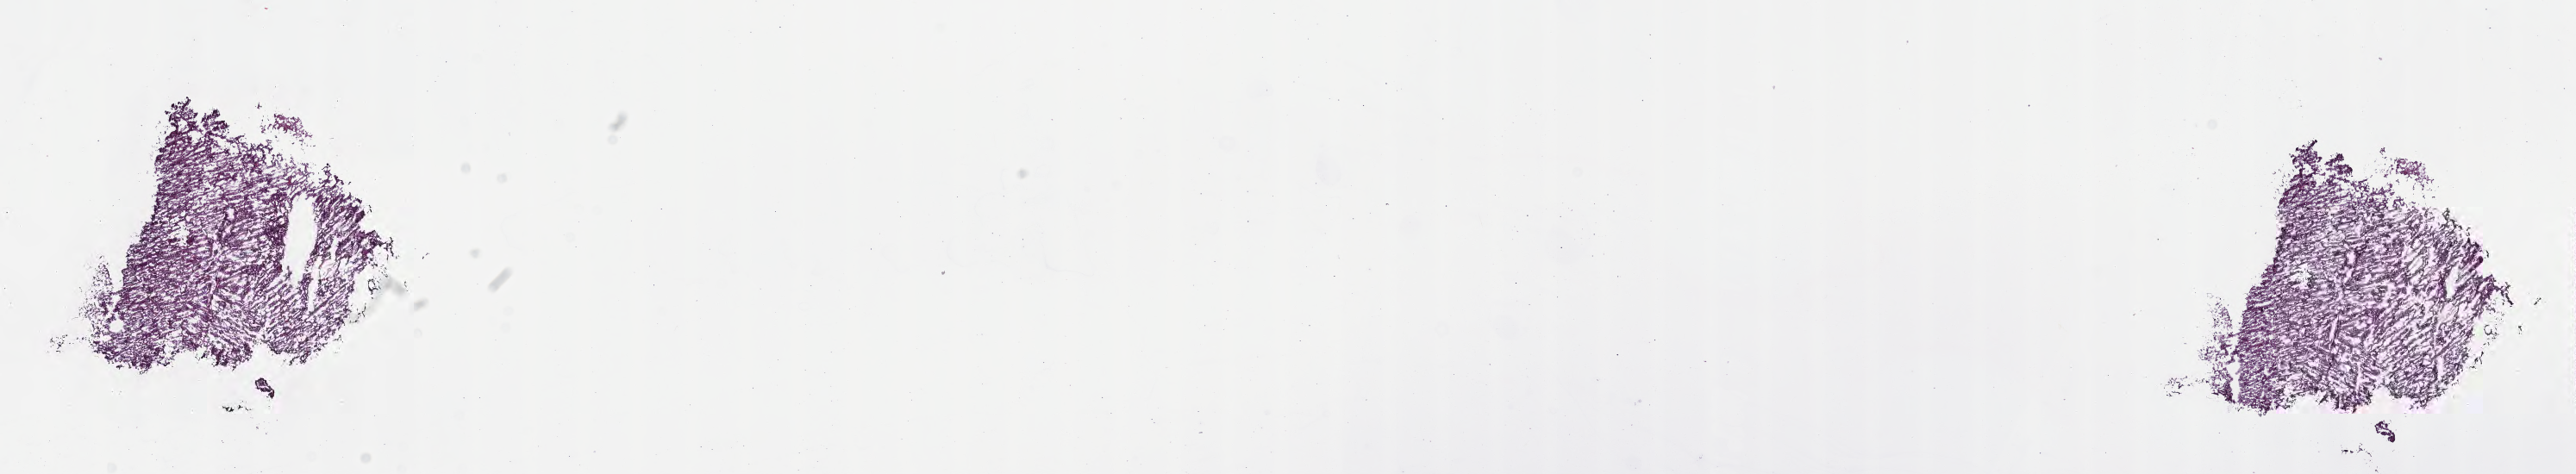
Haematoxylin and eosin whole-slide image of tumor tissue from the brain — whole scanned area (about 24.1 x 4.4 mm) shown as a low-resolution overview. Frozen section (OCT-embedded). Patient female; age 116 days.
Diagnosis: Tumor cells, uncertain whether benign or malignant.